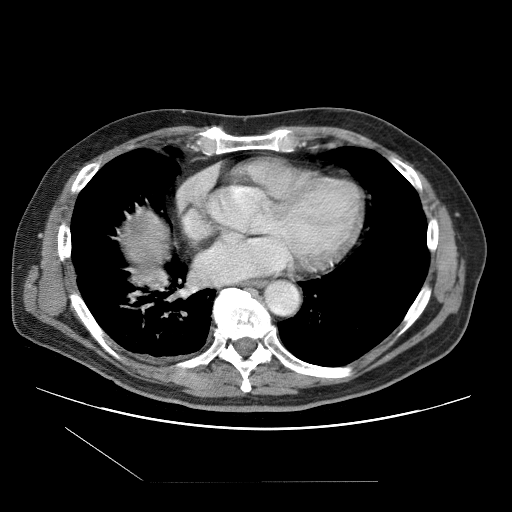
Contrast-enhanced abdominal CT (liver protocol), one axial slice; reconstruction kernel STANDARD; one of 2 acquisitions stored at this slice position; soft-tissue window (W 400 / L 40 HU); 512 × 512 image matrix. From the clinical record (not read from this slice): diagnosis: hepatocellular carcinoma (patient treated with transarterial chemoembolisation; whether this scan precedes or follows treatment is not stated here); TNM stage (as recorded): Stage-IIIB.
Outlined on this slice (semi-automatically segmented with operator editing):
- liver parenchyma outside the tumour (the mass and vessels are separate outlines, so this box may not span the whole liver): bounding box [x1, y1, x2, y2] px = [120, 212, 168, 272]